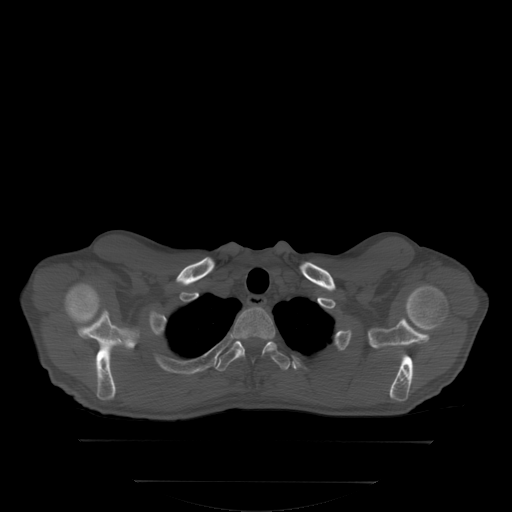
CT including the spine, one axial slice; position 283 of 350 along the scan axis; bone window (W 1800 / L 400 HU); 2.5 mm slice thickness; 512 × 512 image matrix, field of view 500 × 500 mm. Male patient, age 58 years. Case-level facts recorded for this patient, not image findings: primary cancer: prostate.
Structures marked on this image (semi-automatically segmented with operator editing):
- T1 vertebra: bounding box <233,307,276,362> (left, top, right, bottom; pixels)
- T2 vertebra: <214,340,291,374>